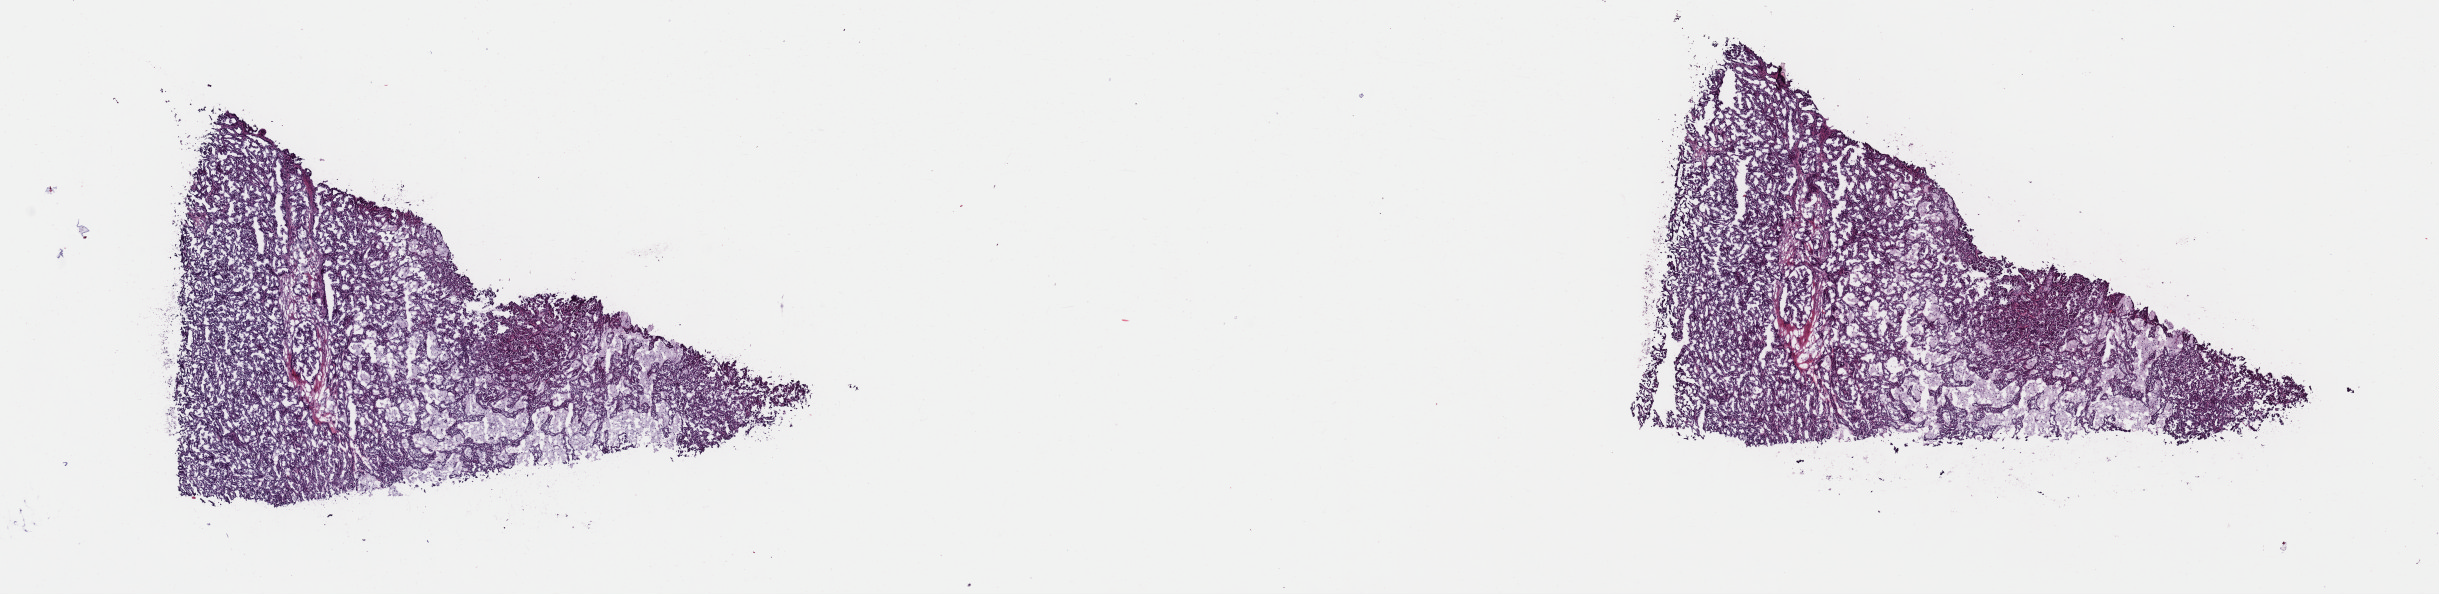
Digitized Hematoxylin and eosin (H&E) stained tissue section (whole slide), low-resolution overview of the scanned area, about 19.3 x 4.7 mm; frozen section; sample: primary tumour, kidney. Male, age 62 years at initial diagnosis. Pathologist review of this section (percent, as recorded): tumour cells 100%, tumour nuclei 75%, normal cells 0%, stromal cells 0%, necrosis 0%. Infiltration values recorded for this section: lymphocyte infiltration 1%, monocyte infiltration 4%, neutrophil infiltration 0%.
- laterality: left
- AJCC pathologic stage: I
- diagnosis: Papillary adenocarcinoma, NOS